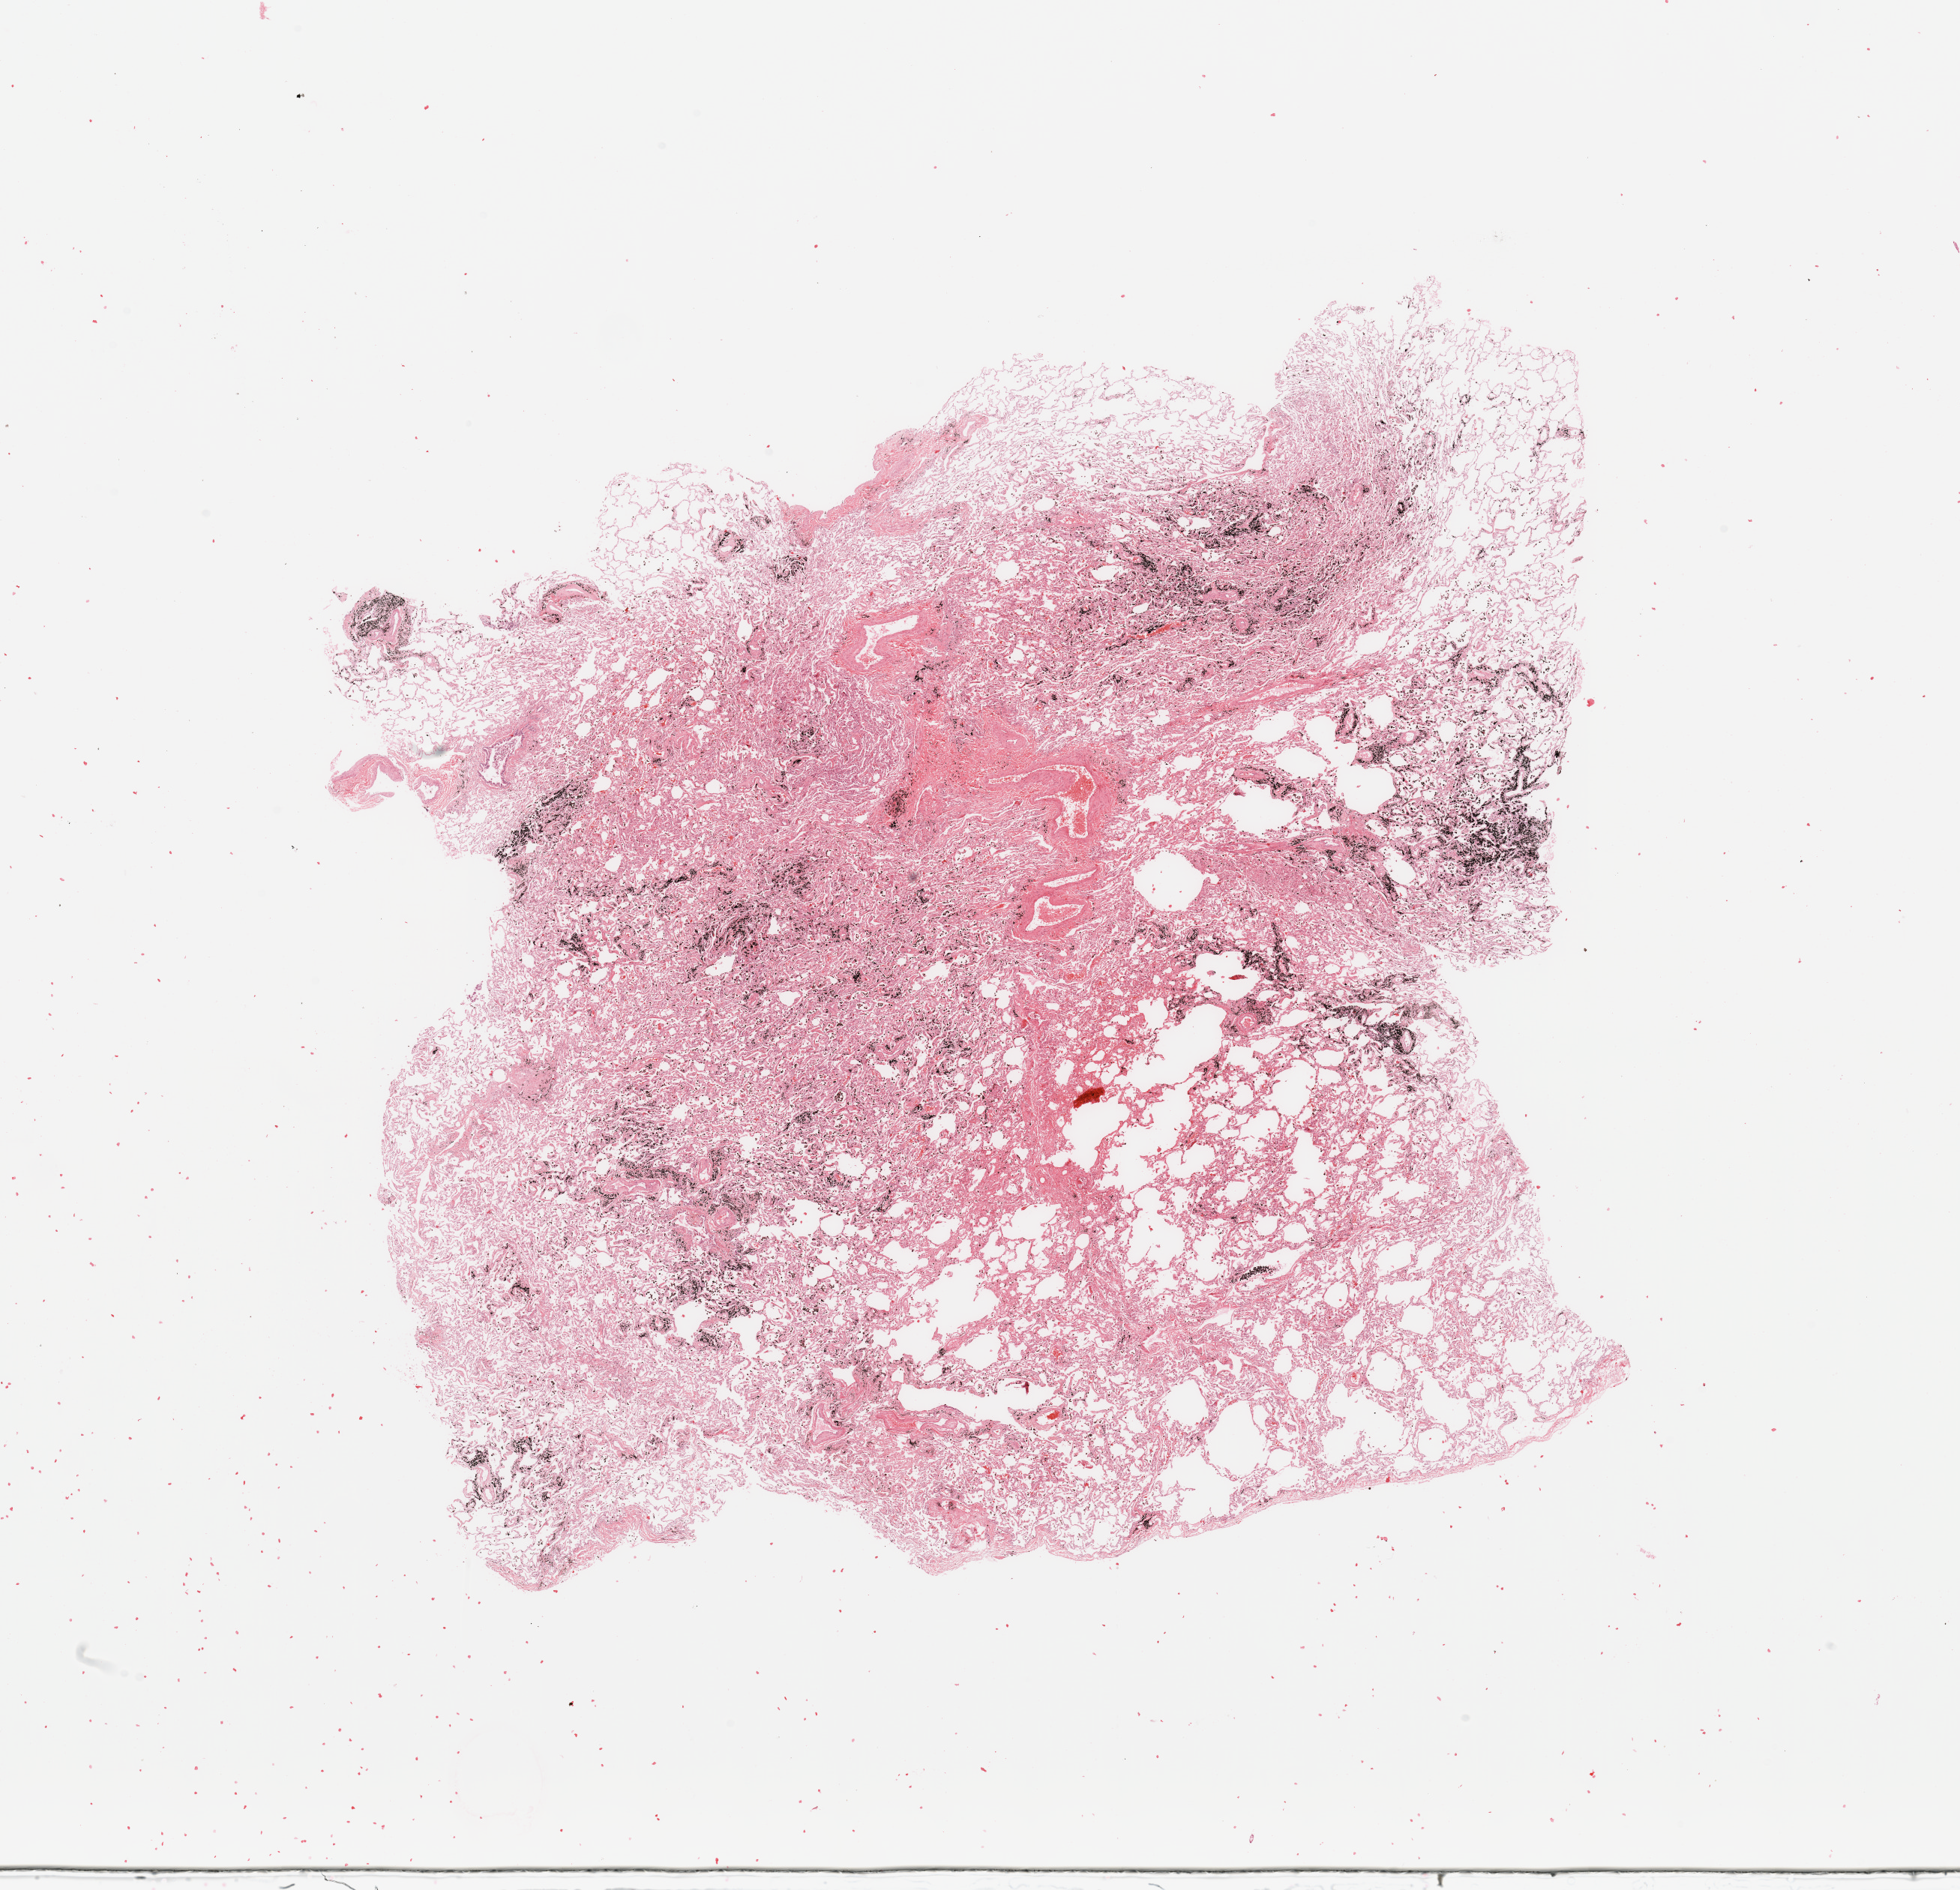
H&E-stained whole-slide image — shown as a low-resolution overview of the whole scanned area (about 20.7 x 19.9 mm, from a 20x scan). Normal (non-tumour) tissue sample, lung. 56-year-old male patient.
This section: normal (non-tumour) tissue from the same patient. Patient diagnosis: Adenocarcinoma, NOS.